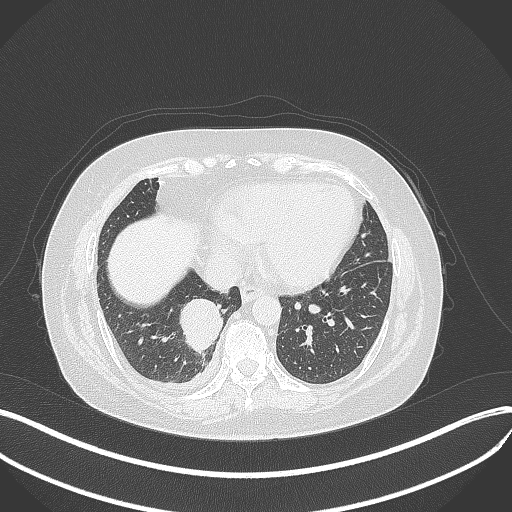
Chest CT, one axial slice; reconstruction kernel B70f; lung window (W 1500 / L -600 HU); 1 mm slice thickness; 512 × 512 image matrix, field of view 400 × 400 mm. Patient: female, 56 years. From the clinical record (not read from this slice): clinical TNM (as recorded): T2b N1 M0; histopathological grade: G3.
Structures marked on this image (rectangle marked by the reading radiologist):
- lung tumour (recorded histology: small cell carcinoma): bounding box [x1, y1, x2, y2] px = [179, 296, 223, 354]